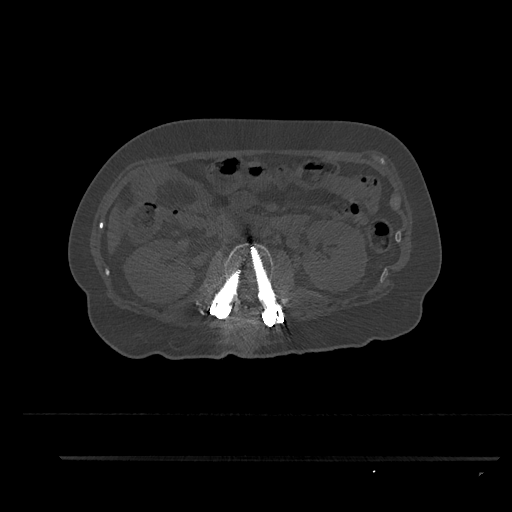
CT including the spine, one axial slice. Slice 166 of 797 in the series (ordered by position). Reconstruction kernel Br40s/3. 120 kVp. Bone window (W 1800 / L 400 HU). 0.5 mm slice thickness. 512 × 512 image matrix, field of view 408 × 408 mm. Female patient, age 44 years. Case-level facts recorded for this patient, not image findings: primary cancer: renal; vertebrae with lytic lesions (as recorded): L1.
Structures marked on this image (semi-automatic segmentation, software-assisted and operator-edited):
- L2 vertebra: box from (x=206, y=243) to (x=285, y=320) px